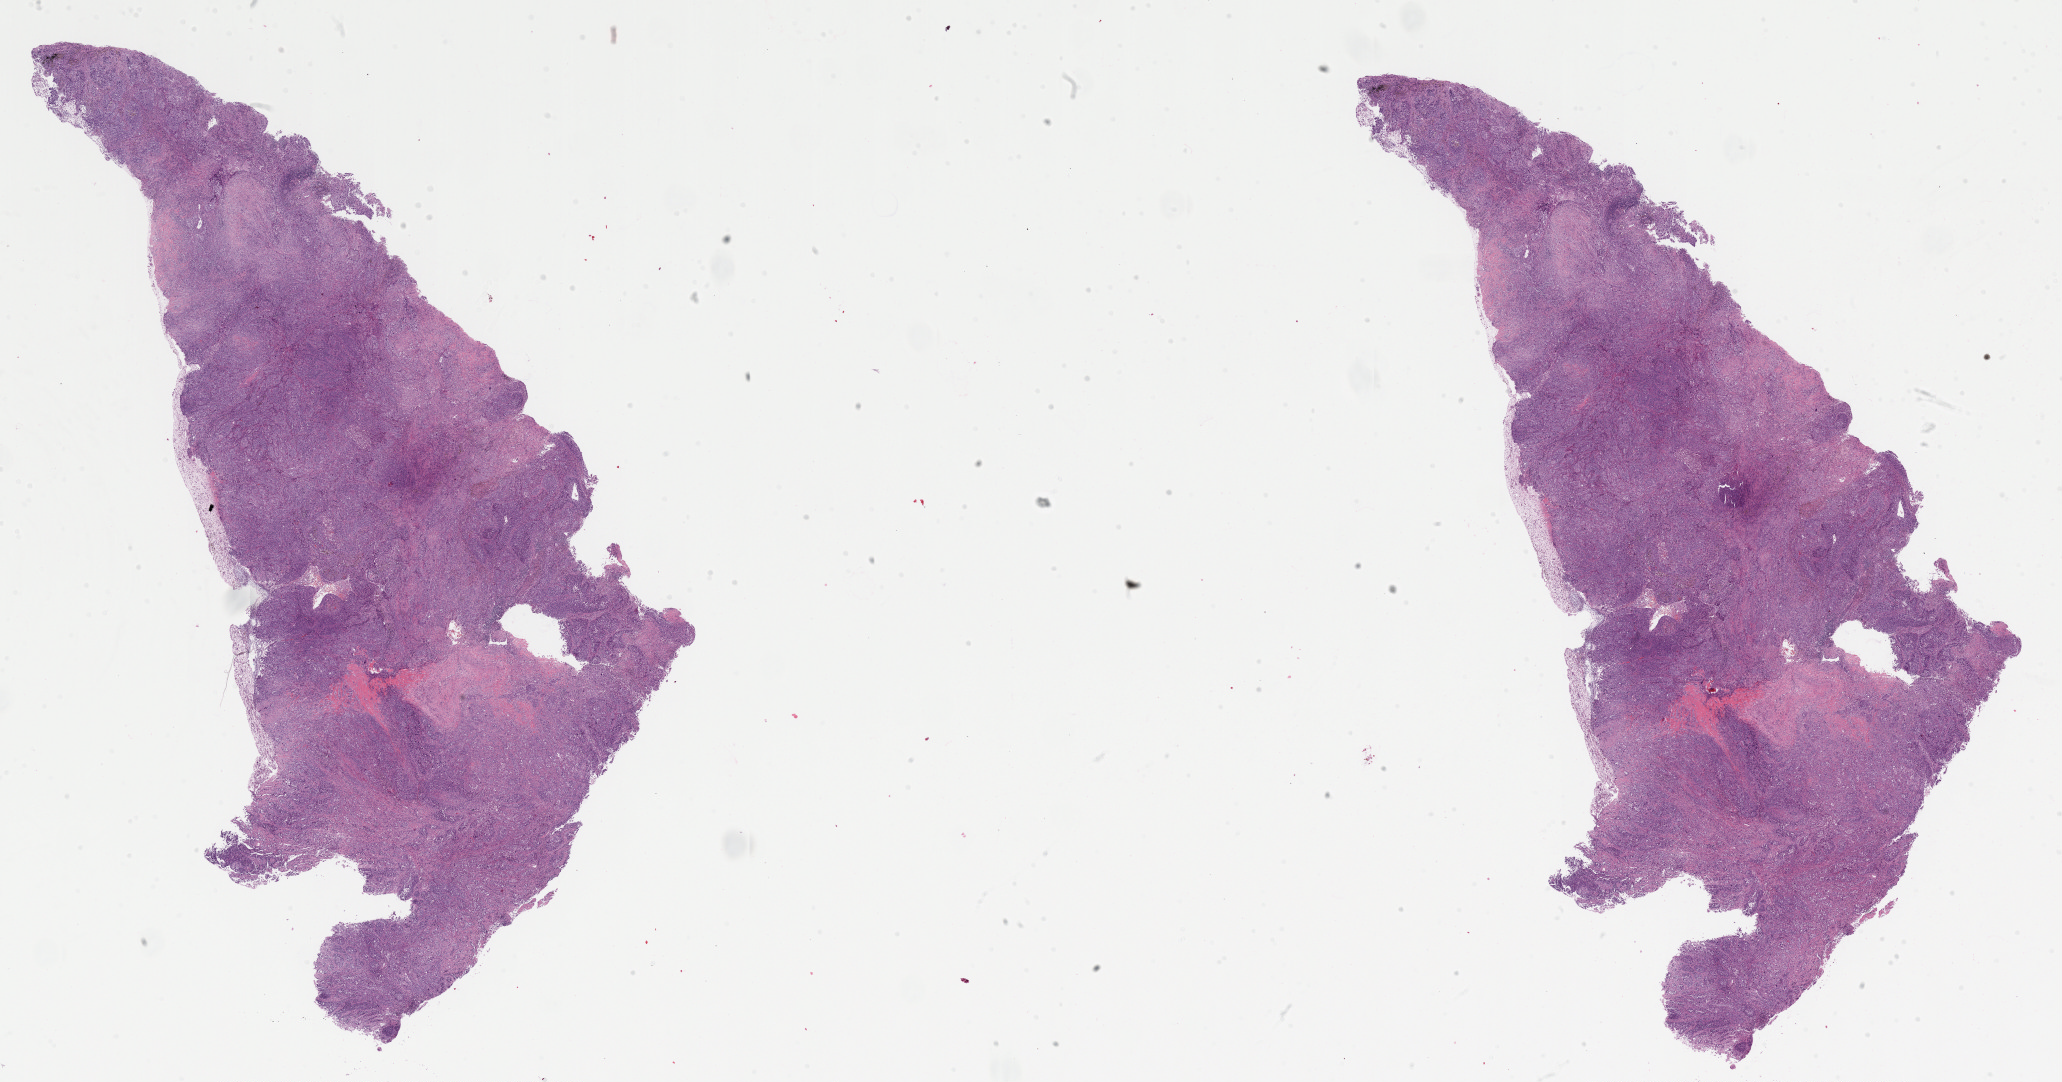
H&E whole-slide image — low-resolution overview of the scanned area, about 33.0 x 17.3 mm (acquisition: 20x scan), formalin-fixed paraffin-embedded (FFPE) diagnostic section, sample: primary tumour, lung. Male patient; age at initial diagnosis 74 years.
AJCC pathologic stage: IIB (7th edition). Diagnosis: Squamous cell carcinoma, NOS (upper lobe, lung). TNM: T3 N0 M0. Laterality: right.